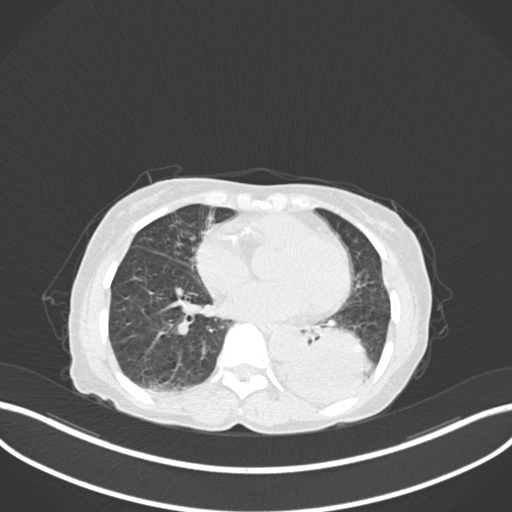
Chest CT, one axial slice. Slice 50 of 233 in the series (ordered by position). 120 kVp. Lung window (W 1500 / L -600 HU). 1 mm slice thickness. 512 × 512 image matrix. Female patient, age 78 years. From the clinical record (not read from this slice): clinical TNM (as recorded): T3 N0 M1.
Structures marked on this image (bounding box drawn by a radiologist):
- lung tumour (recorded histology: squamous cell carcinoma): bounding box [x1, y1, x2, y2] px = [278, 321, 372, 408]